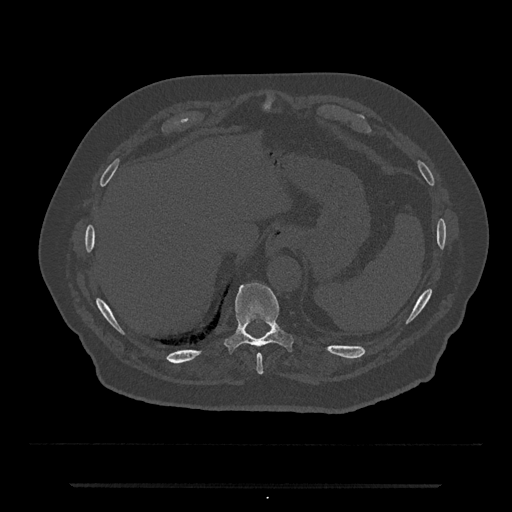
CT including the spine, one axial slice; slice 711 of 797 in the series (ordered by position); reconstruction kernel Br40s/3; 120 kVp; bone window (W 1800 / L 400 HU); 0.5 mm slice thickness; 512 × 512 image matrix. Patient: male, 80 years. From the clinical record (not read from this slice): primary cancer: prostate.
Annotated regions visible in this slice (semi-automatic segmentation, software-assisted and operator-edited):
- T10 vertebra: bounding box [x1, y1, x2, y2] px = [225, 283, 293, 352]
- T9 vertebra: [257, 354, 264, 375]